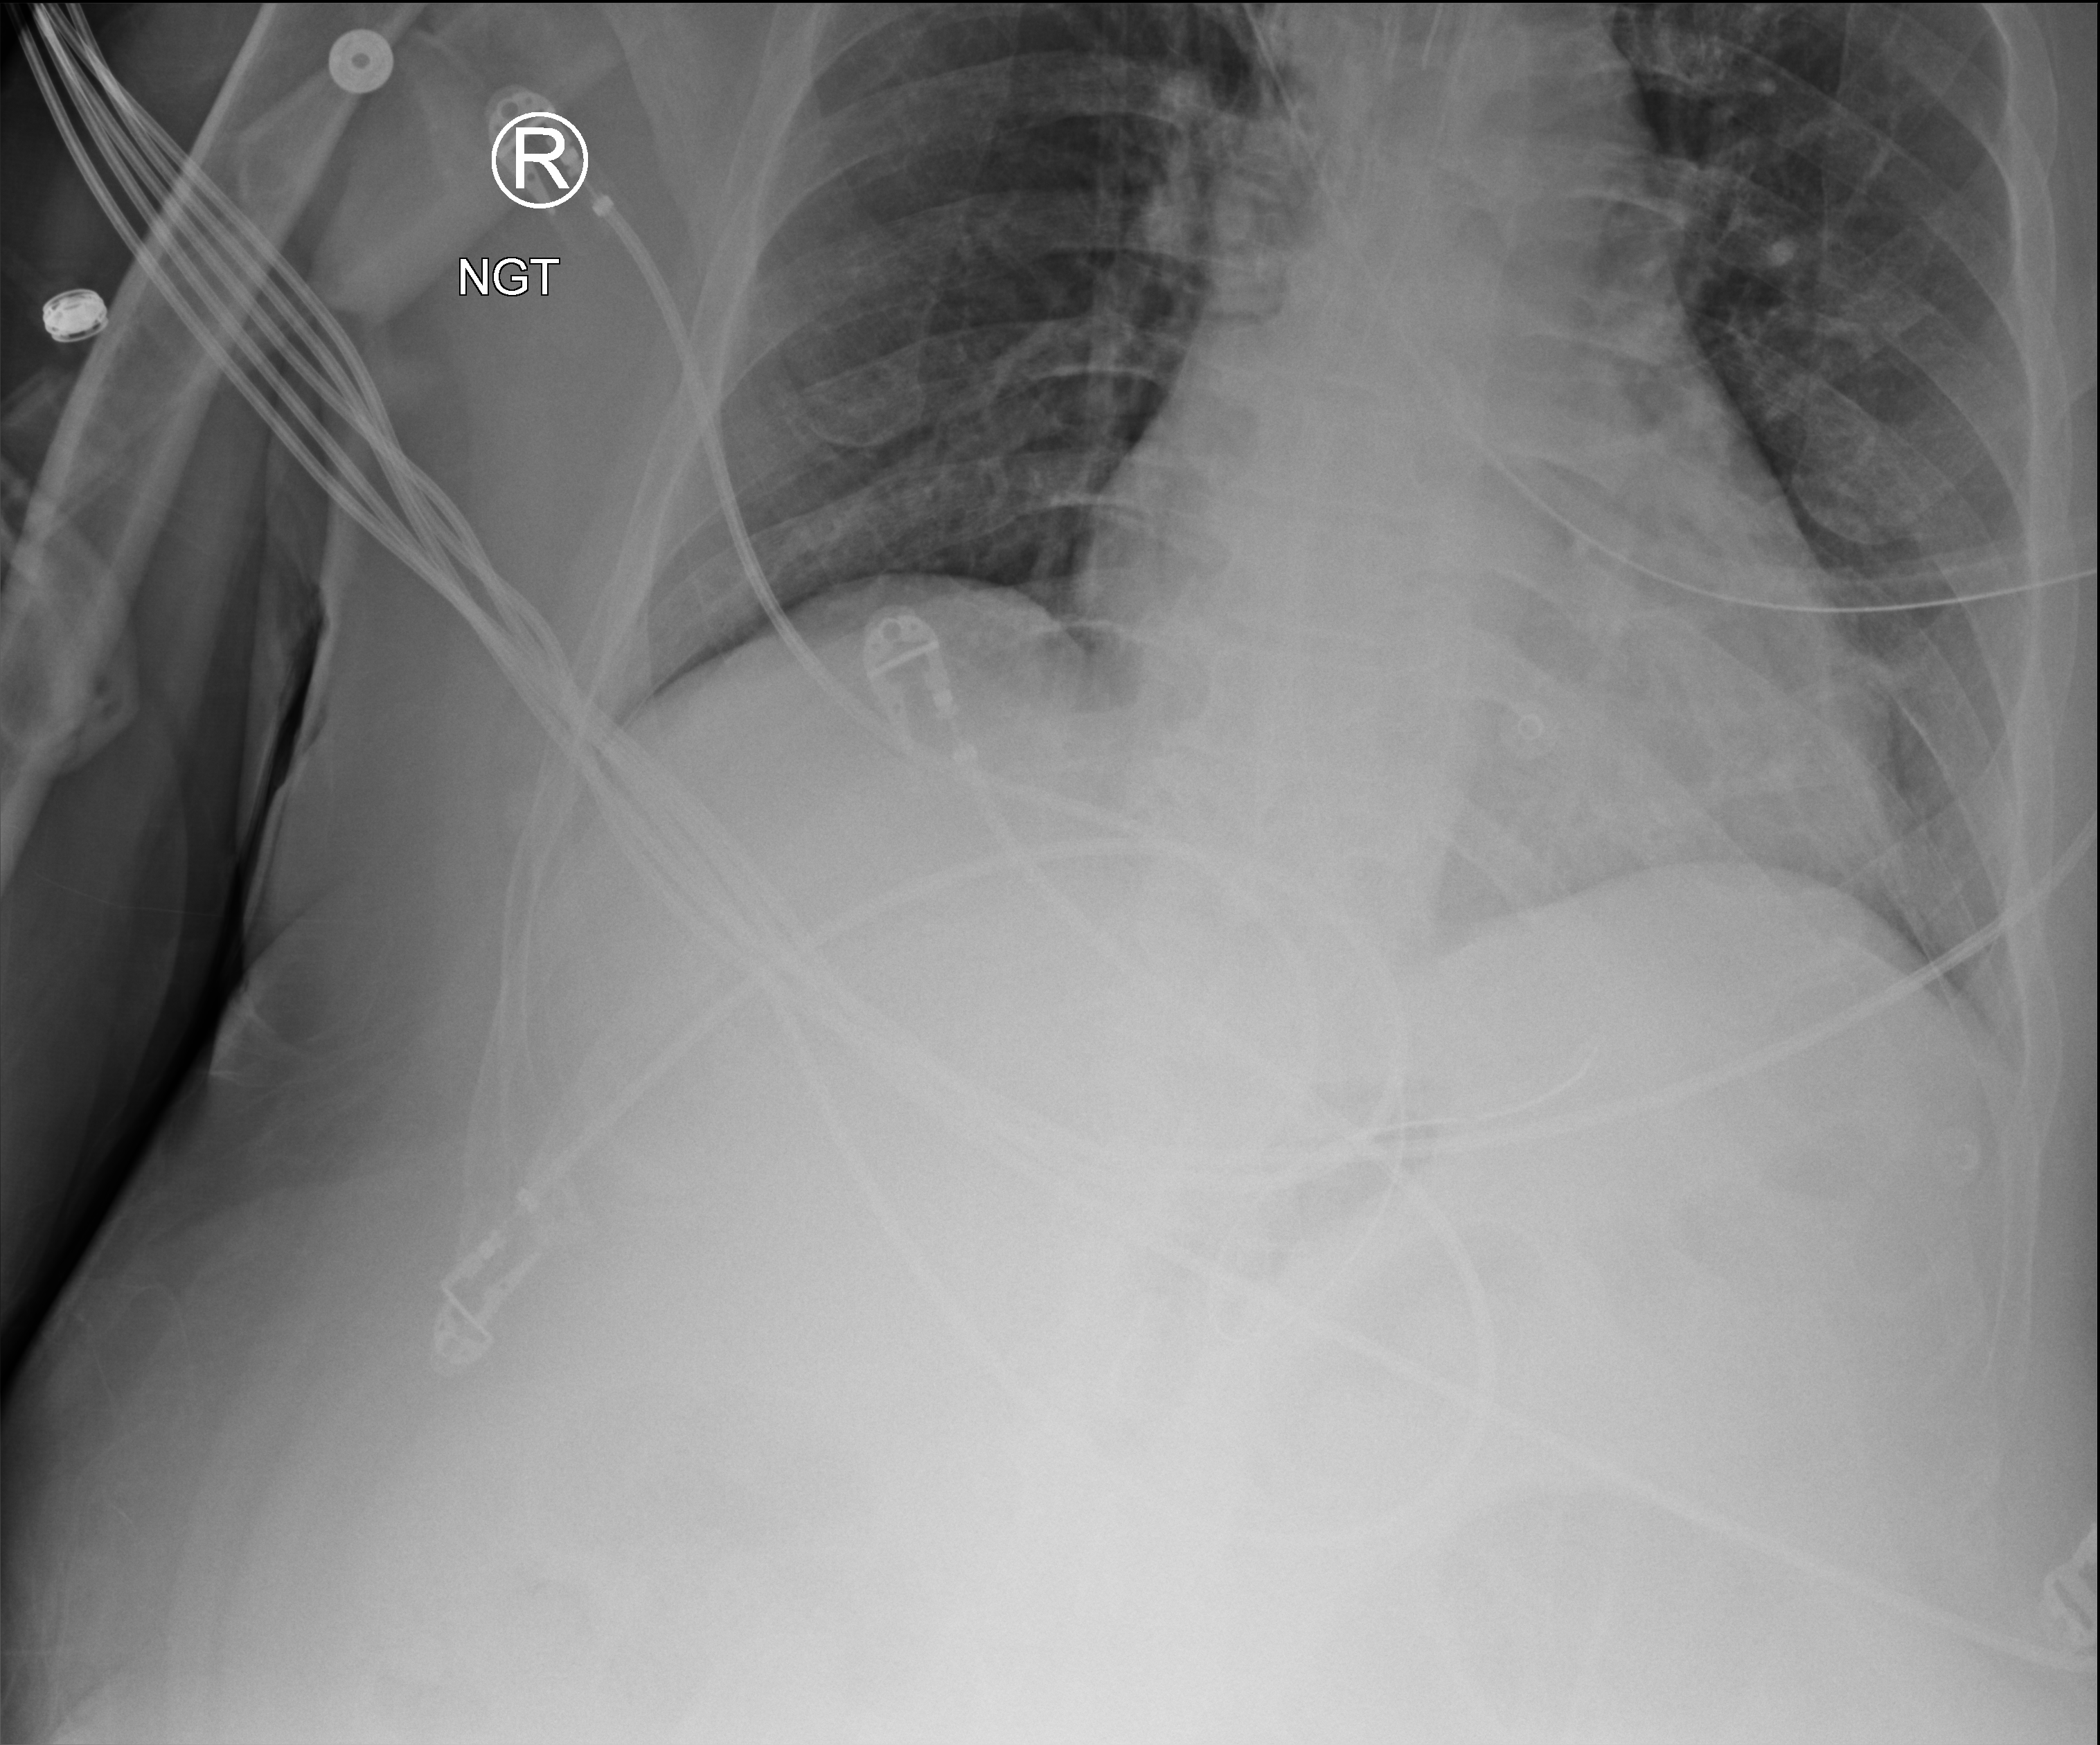
Chest X-ray (portable), anteroposterior (AP) projection. Patient hospitalised with COVID-19, aged 18–59 years.
From the hospital-stay record, not from the radiograph (when in the stay this image was taken is not recorded):
- admitted to intensive care during this hospital stay: yes
- mechanically ventilated during this hospital stay: yes